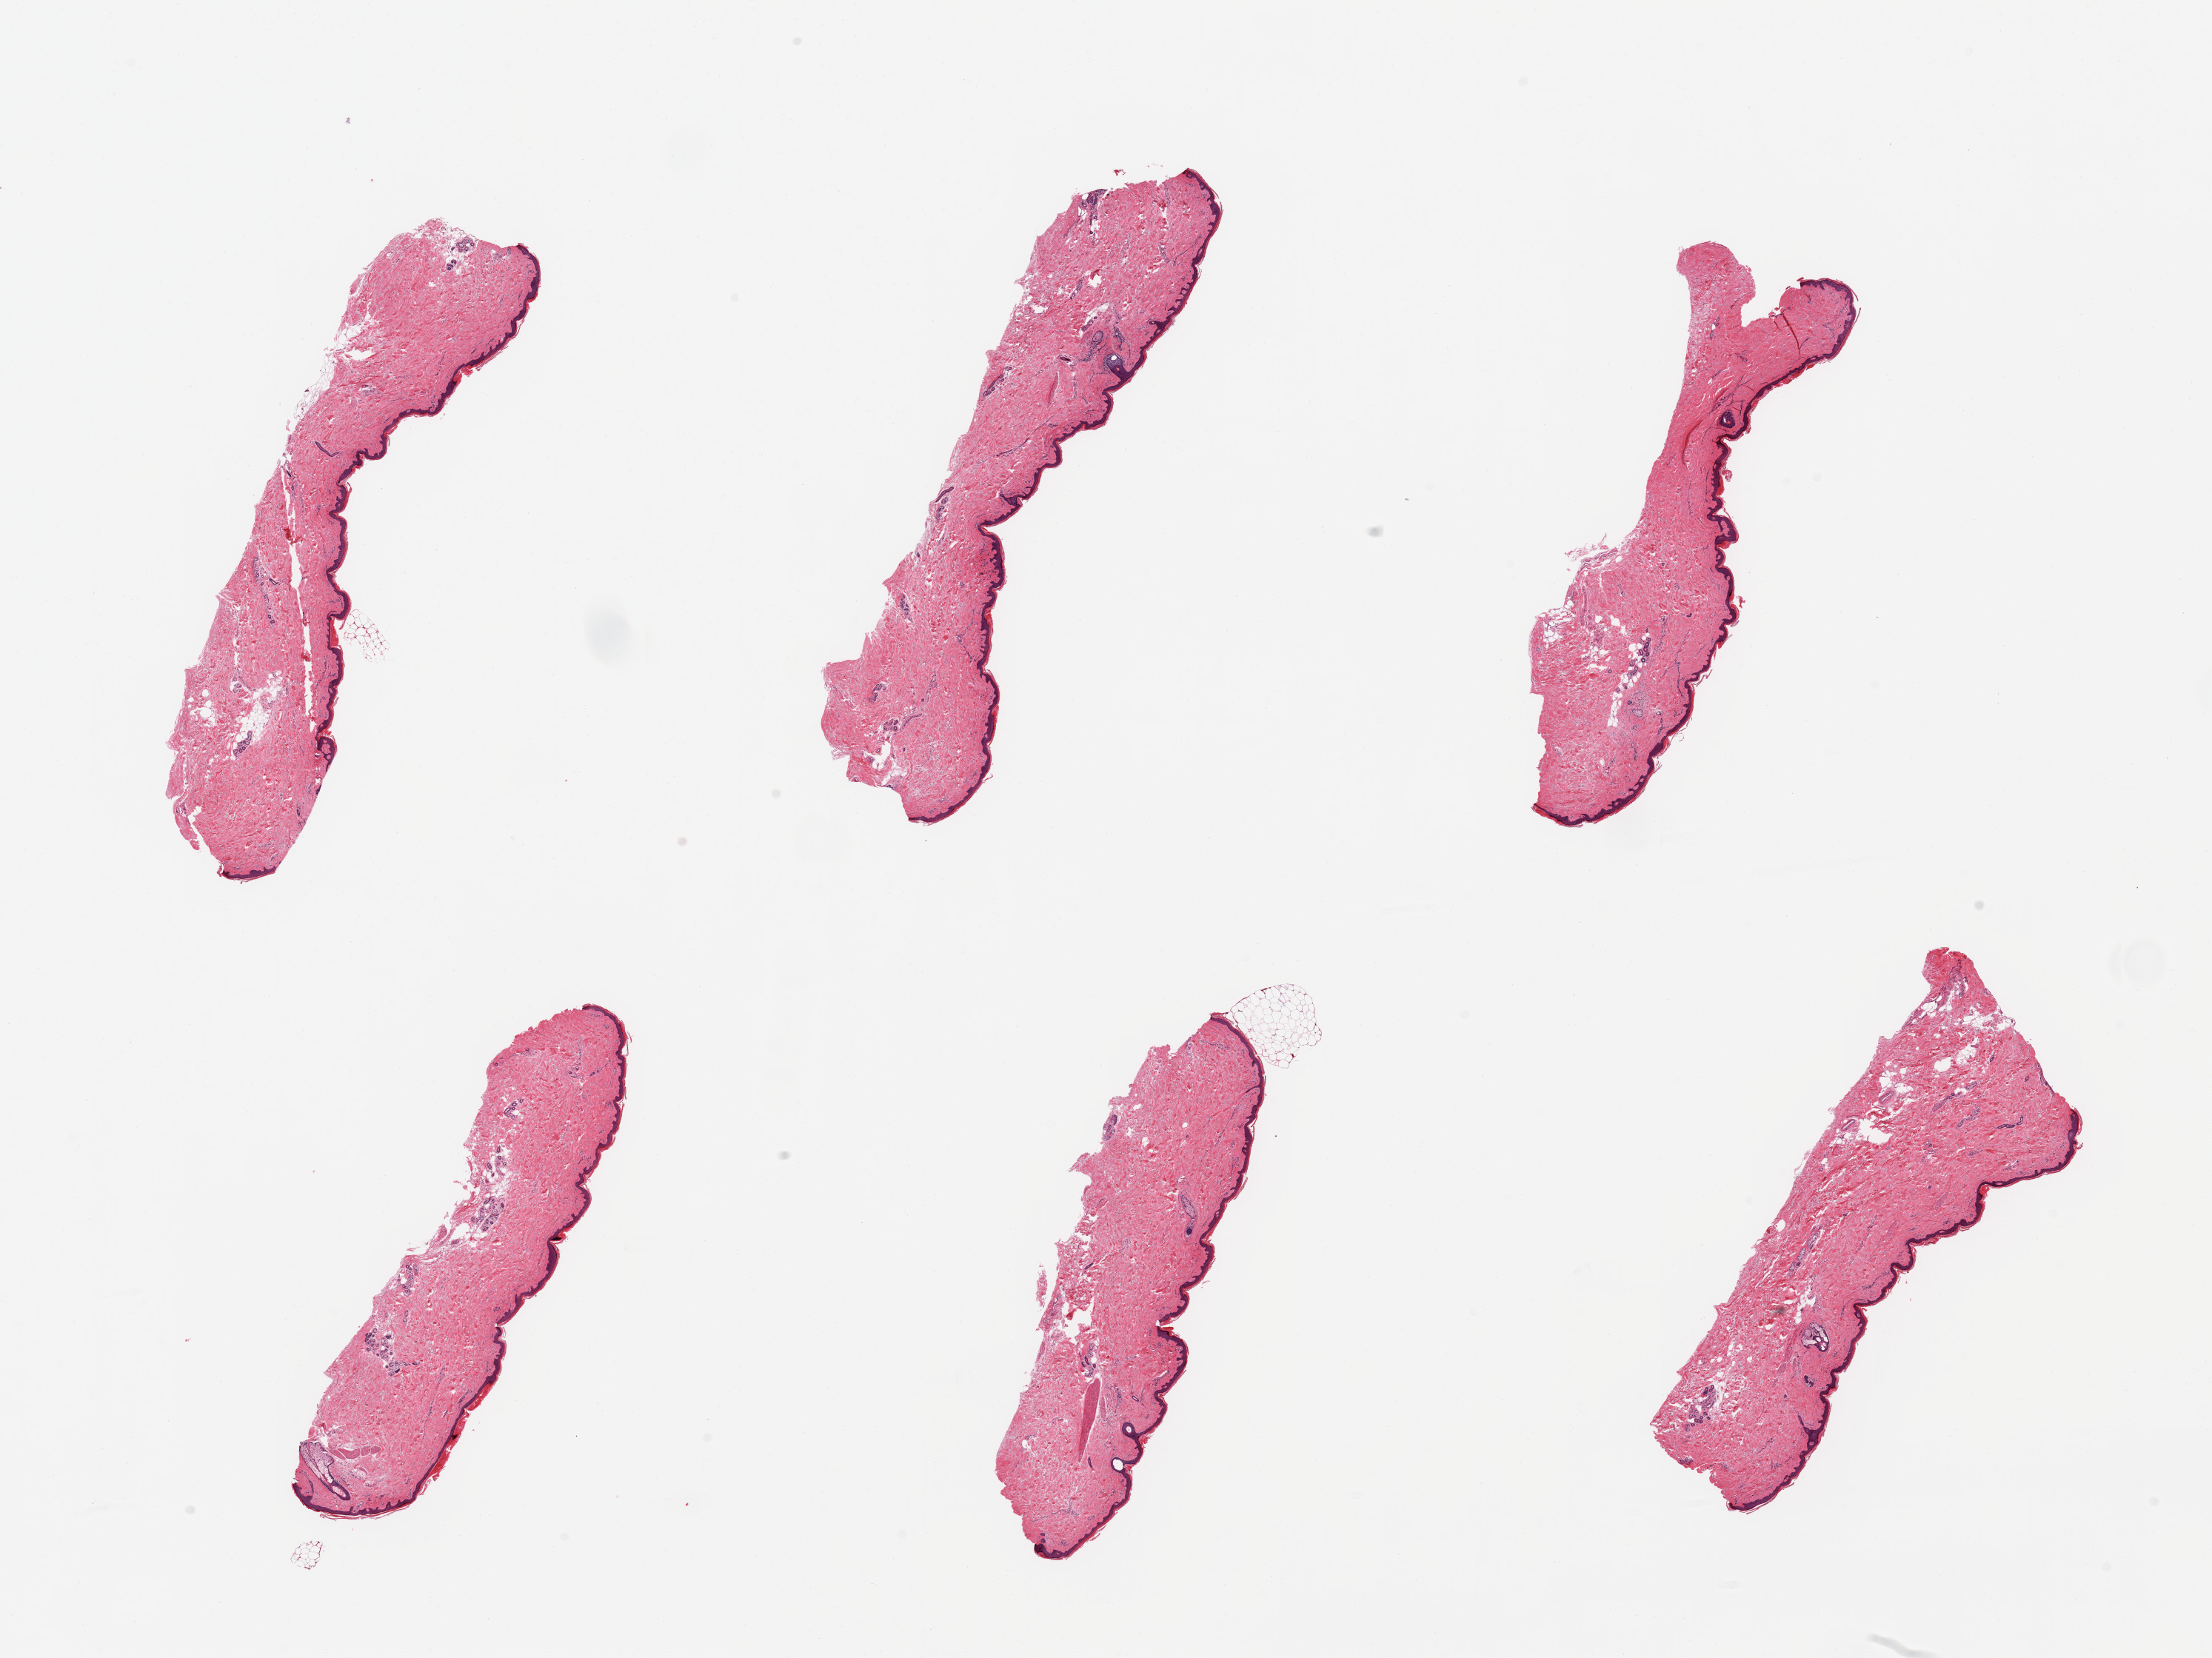
Digitized haematoxylin and eosin-stained section, brightfield — a low-resolution overview of the entire scanned area, about 23.6 x 17.7 mm, PAXgene-fixed paraffin-embedded (PFPE) section, section of skin of lower leg (target tissue), donor tissue sample.
Reviewer comment on this tissue sample: 6 pieces, no dermal fat; squamous epithelium is ~40 microns.